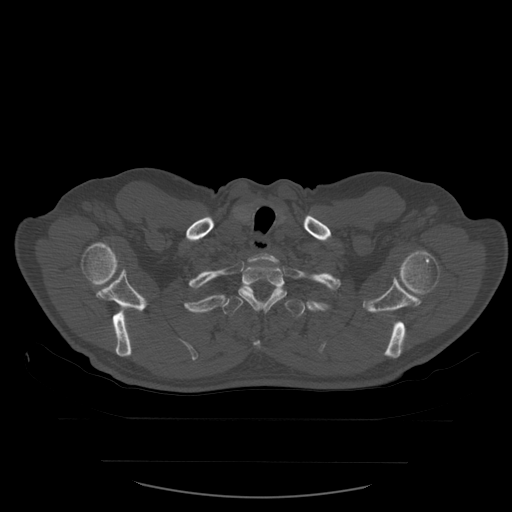
CT including the spine, one axial slice; position 471 of 590 along the scan axis; bone window (W 1800 / L 400 HU); 1.25 mm slice thickness; 512 × 512 image matrix, field of view 479 × 479 mm. Patient age 71 years. Case-level facts recorded for this patient, not image findings: primary cancer: lung.
Annotated regions visible in this slice (semi-automatically segmented with operator editing):
- T1 vertebra: bounding box <248,253,281,270> (left, top, right, bottom; pixels)
- T2 vertebra: <239,262,287,312>
- T3 vertebra: <221,290,306,350>